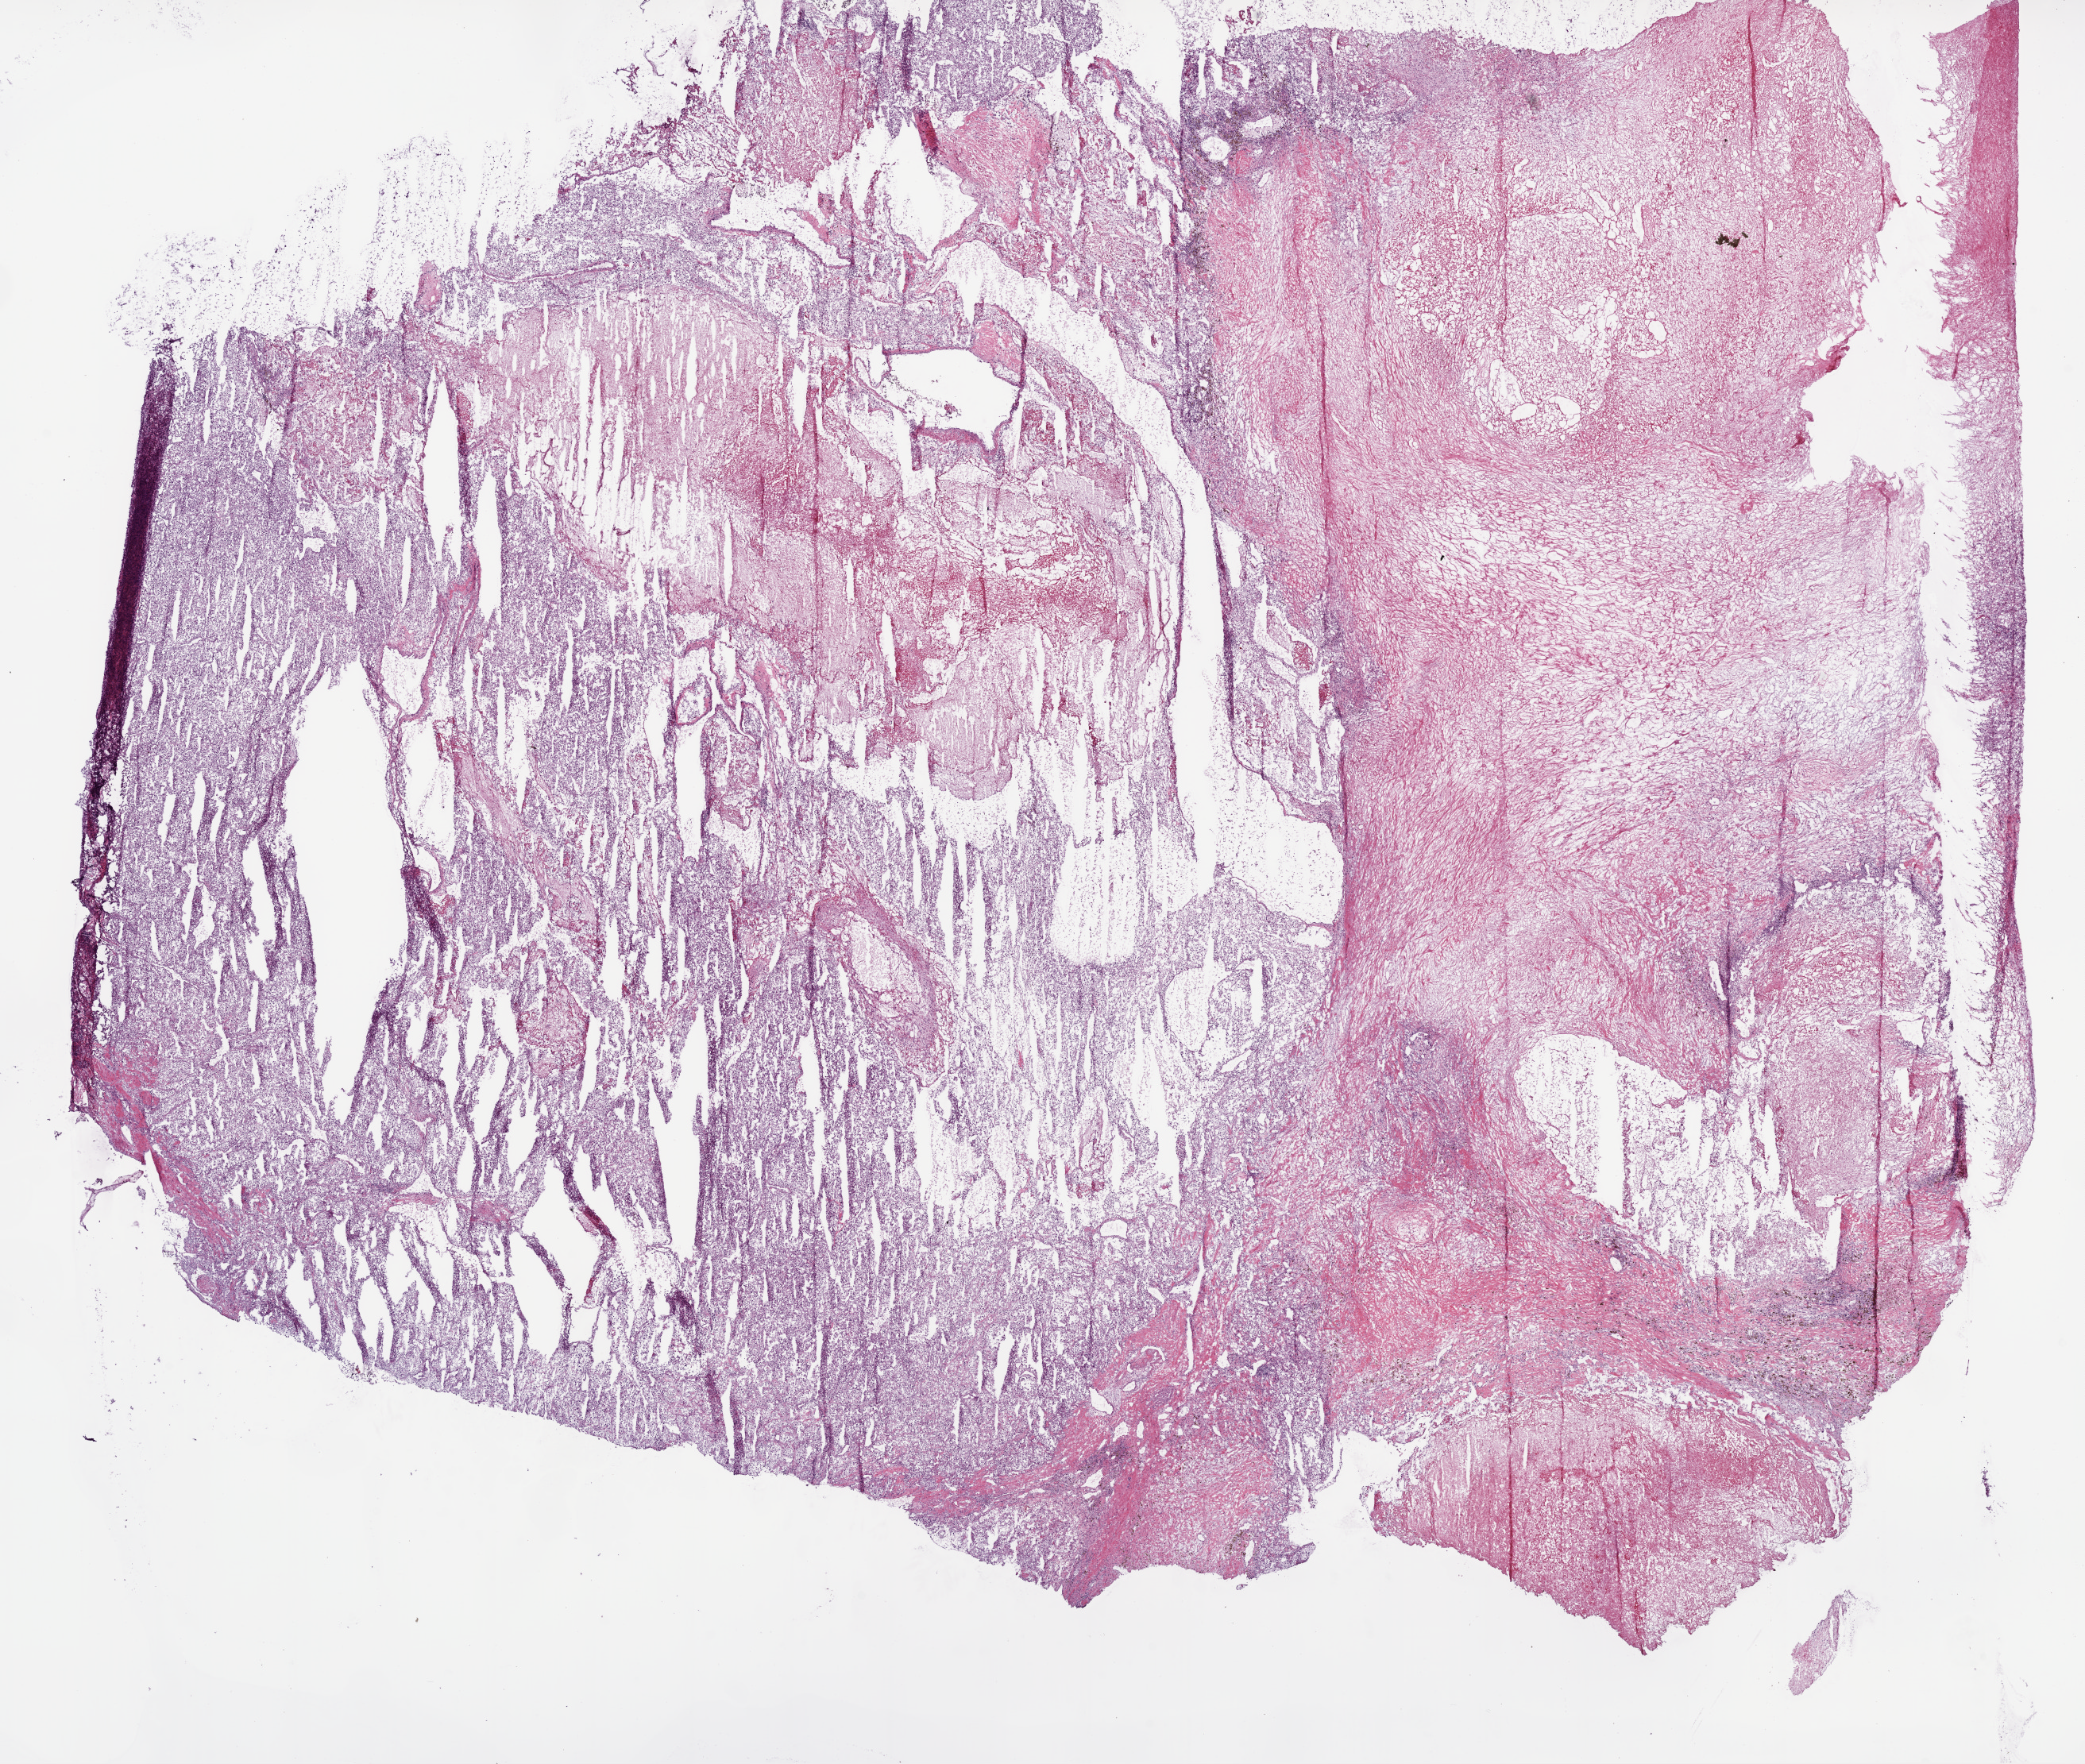
Digitized Hematoxylin and eosin (H&E) stained tissue section (whole slide), a low-resolution overview of the entire scanned area, about 21.1 x 17.8 mm (from a 20x scan), frozen section from the bottom of the tissue portion, primary tumour sample from the kidney. Patient: male, age at initial diagnosis 72 years. Histologic grade: G3 (poorly differentiated). Slide review estimates, as recorded: tumour cells 45%, tumour nuclei 80%, normal cells 0%, stromal cells 45%, necrosis 10%.
* AJCC pathologic stage: III
* pathologic diagnosis: Clear cell adenocarcinoma, NOS
* lymph nodes positive (case pathology): 0 of 9 examined